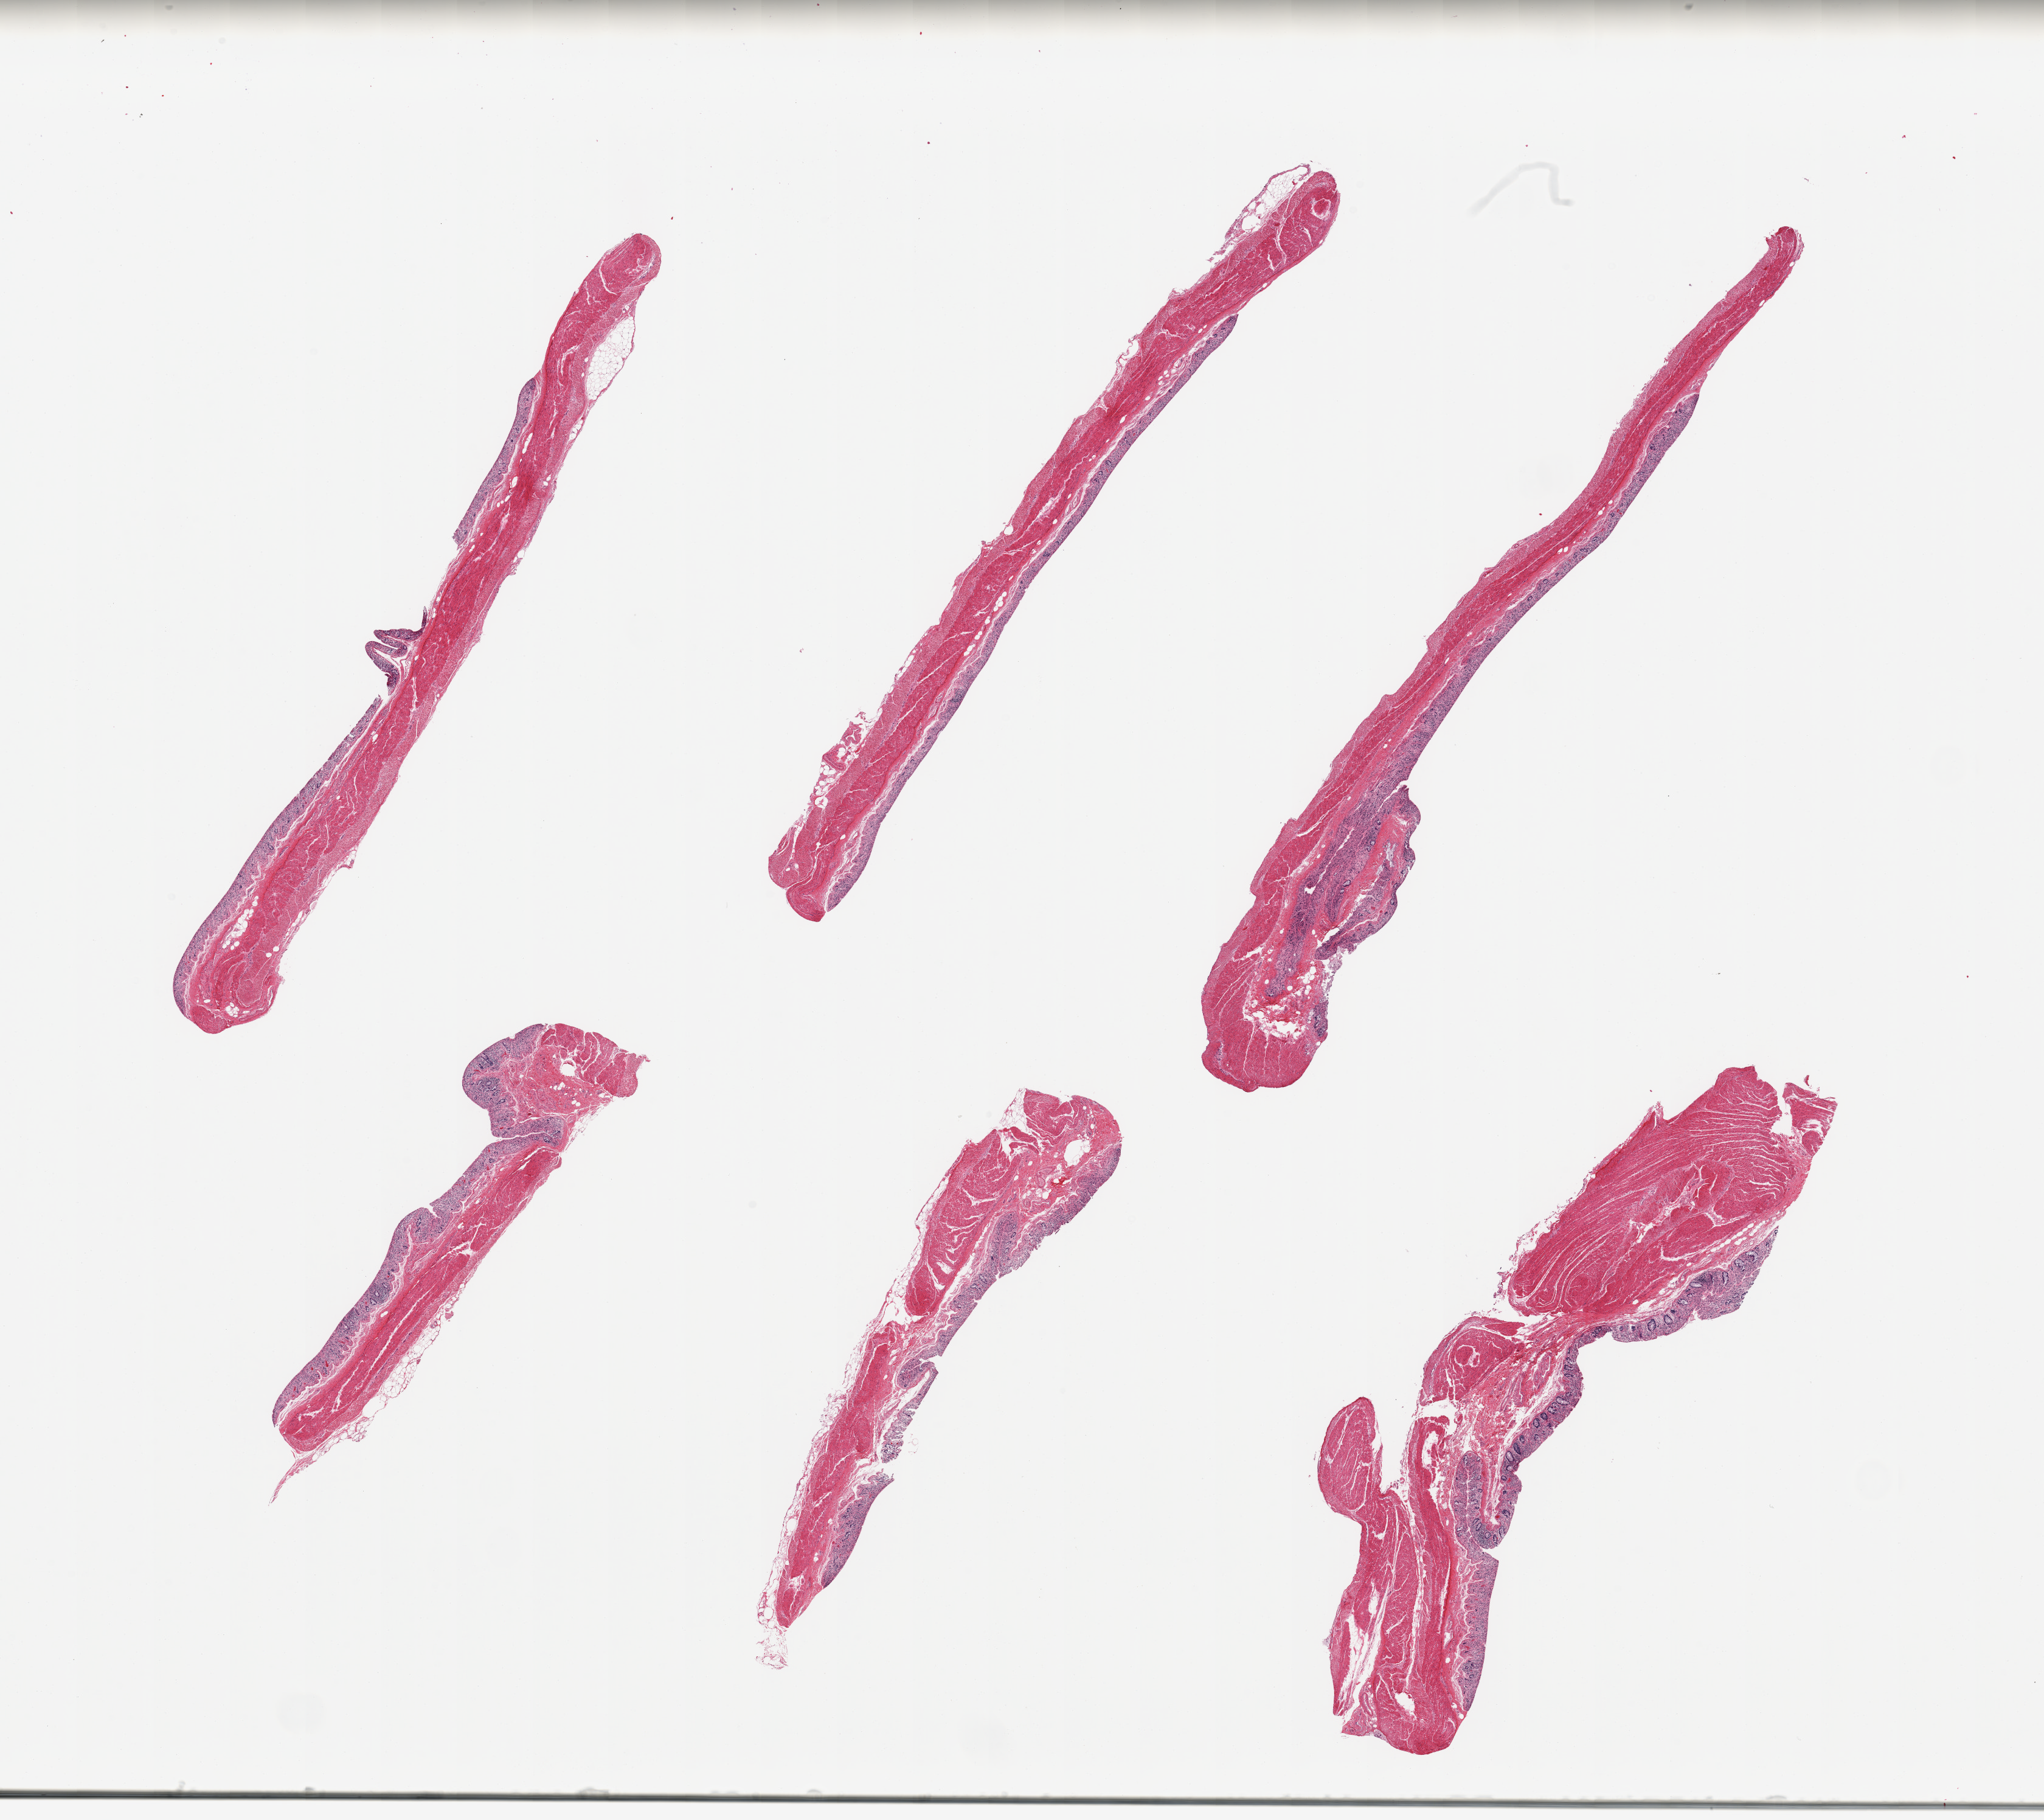
Whole-slide image, H&E stain, brightfield — shown as a low-resolution overview of the whole scanned area (about 26.6 x 23.7 mm, slide scanned at 20x); PAXgene-fixed, paraffin-embedded tissue; target tissue: transverse colon; donor tissue sample. Donor: male.
* review note (as recorded): 6 pieces; mucosa larely autolyzed, muscle intact